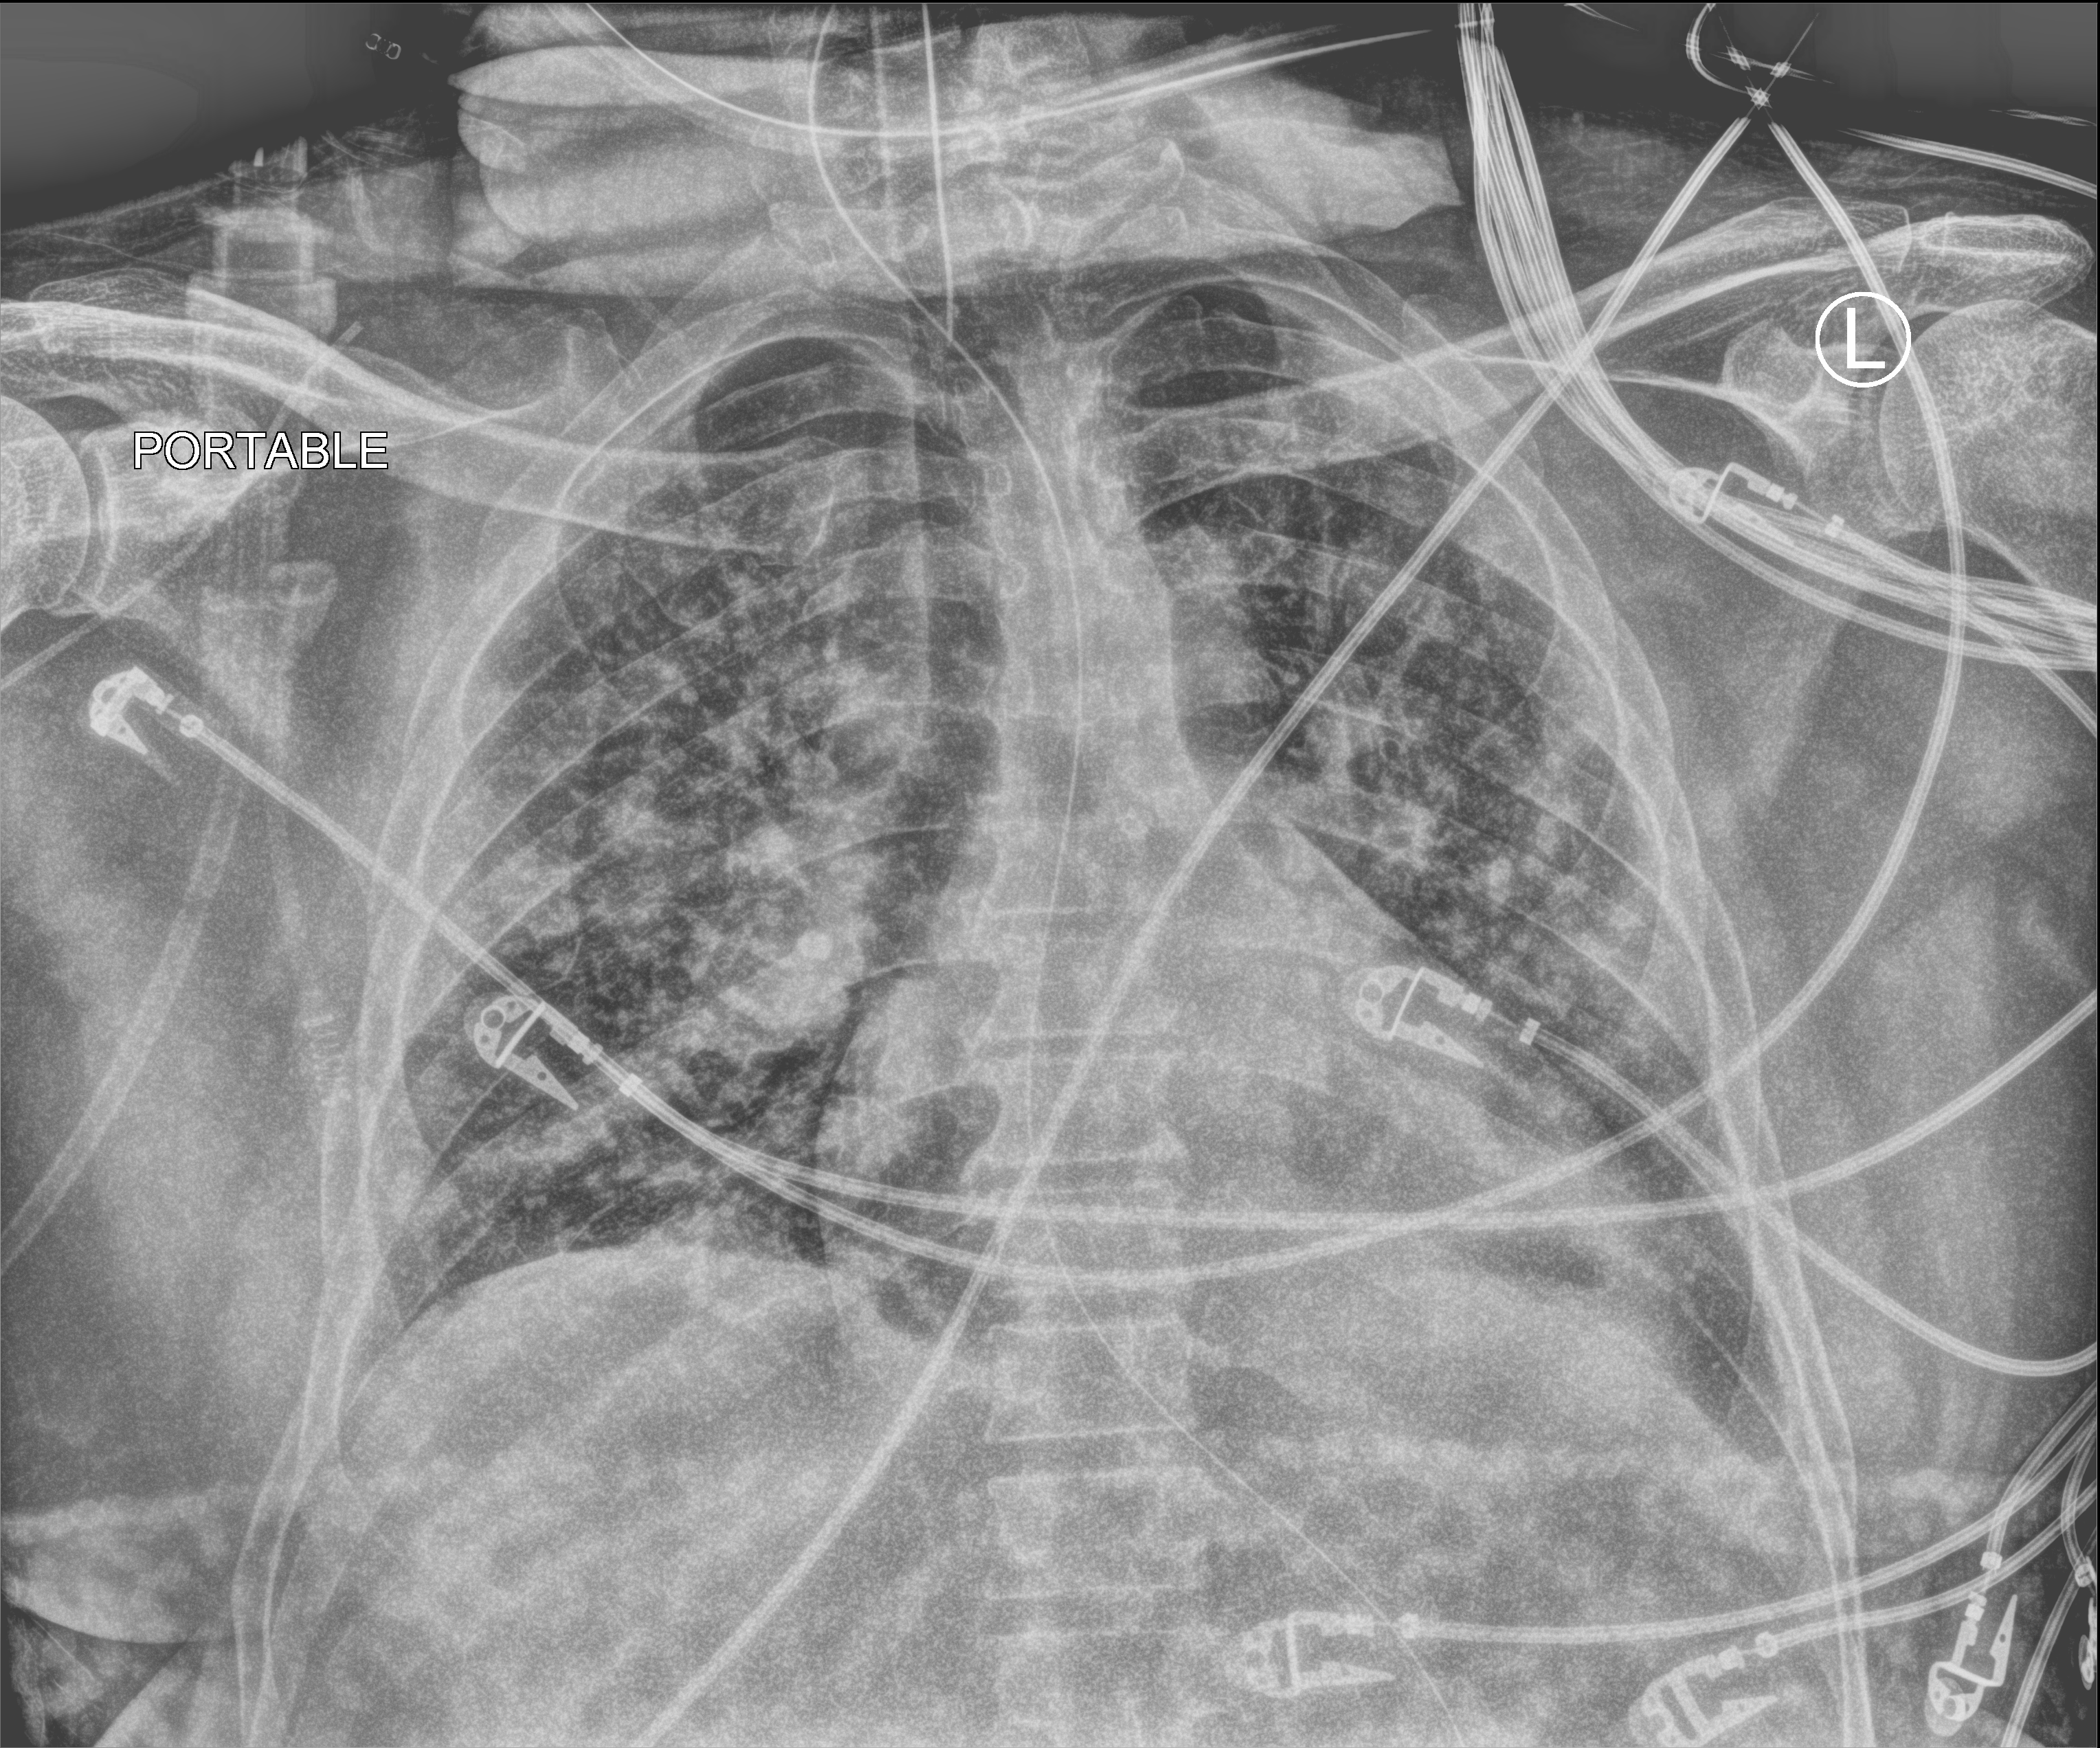
Chest X-ray (portable); anteroposterior (AP) projection. Male patient hospitalised with COVID-19, age 18–59 years.
From the hospital-stay record, not from the radiograph (when in the stay this image was taken is not recorded): mechanically ventilated during this hospital stay: yes.